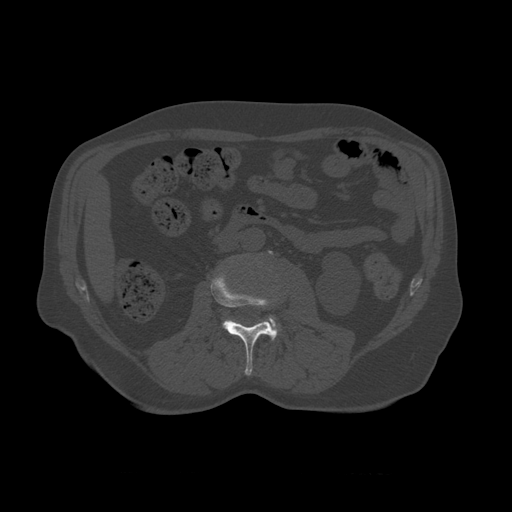
CT including the spine, one axial slice; slice 323 of 450 in the series (ordered by position); 120 kVp; bone window (W 1800 / L 400 HU); 1.25 mm slice thickness; 512 × 512 image matrix, field of view 405 × 405 mm. Patient age 75 years. From the clinical record (not read from this slice): primary cancer: prostate.
Annotated regions visible in this slice (semi-automatic segmentation, software-assisted and operator-edited):
- L2 vertebra: bounding box [x1, y1, x2, y2] px = [211, 267, 281, 376]
- L3 vertebra: [268, 251, 281, 339]